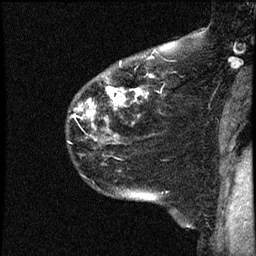
Breast MRI (dynamic contrast-enhanced), one sagittal slice. Position 37 of 44 along the scan axis. Dynamic contrast-enhanced study with each time point stored as its own series, time point 2 of 4 at this slice position (early post-contrast, ordered by acquisition time). 1.5 T. TE 4.2 ms, TR 17.7 ms. 256 × 256 image matrix, field of view 200 × 200 mm. Patient: female, 52 years. From the clinical record (not read from this slice): setting: breast cancer imaged before/during neoadjuvant chemotherapy; receptor status: HR-positive, HER2-negative.
Outlined on this slice (semi-automatic segmentation, software-assisted and operator-edited):
- analysis volume of interest (the breast-tissue region the enhancement analysis was run in; not a lesion): bounding box <66,48,163,147> (left, top, right, bottom; pixels)
- tumour enhancement mask (voxels above the 100 % enhancement threshold inside the analysis volume of interest): <74,55,154,119>